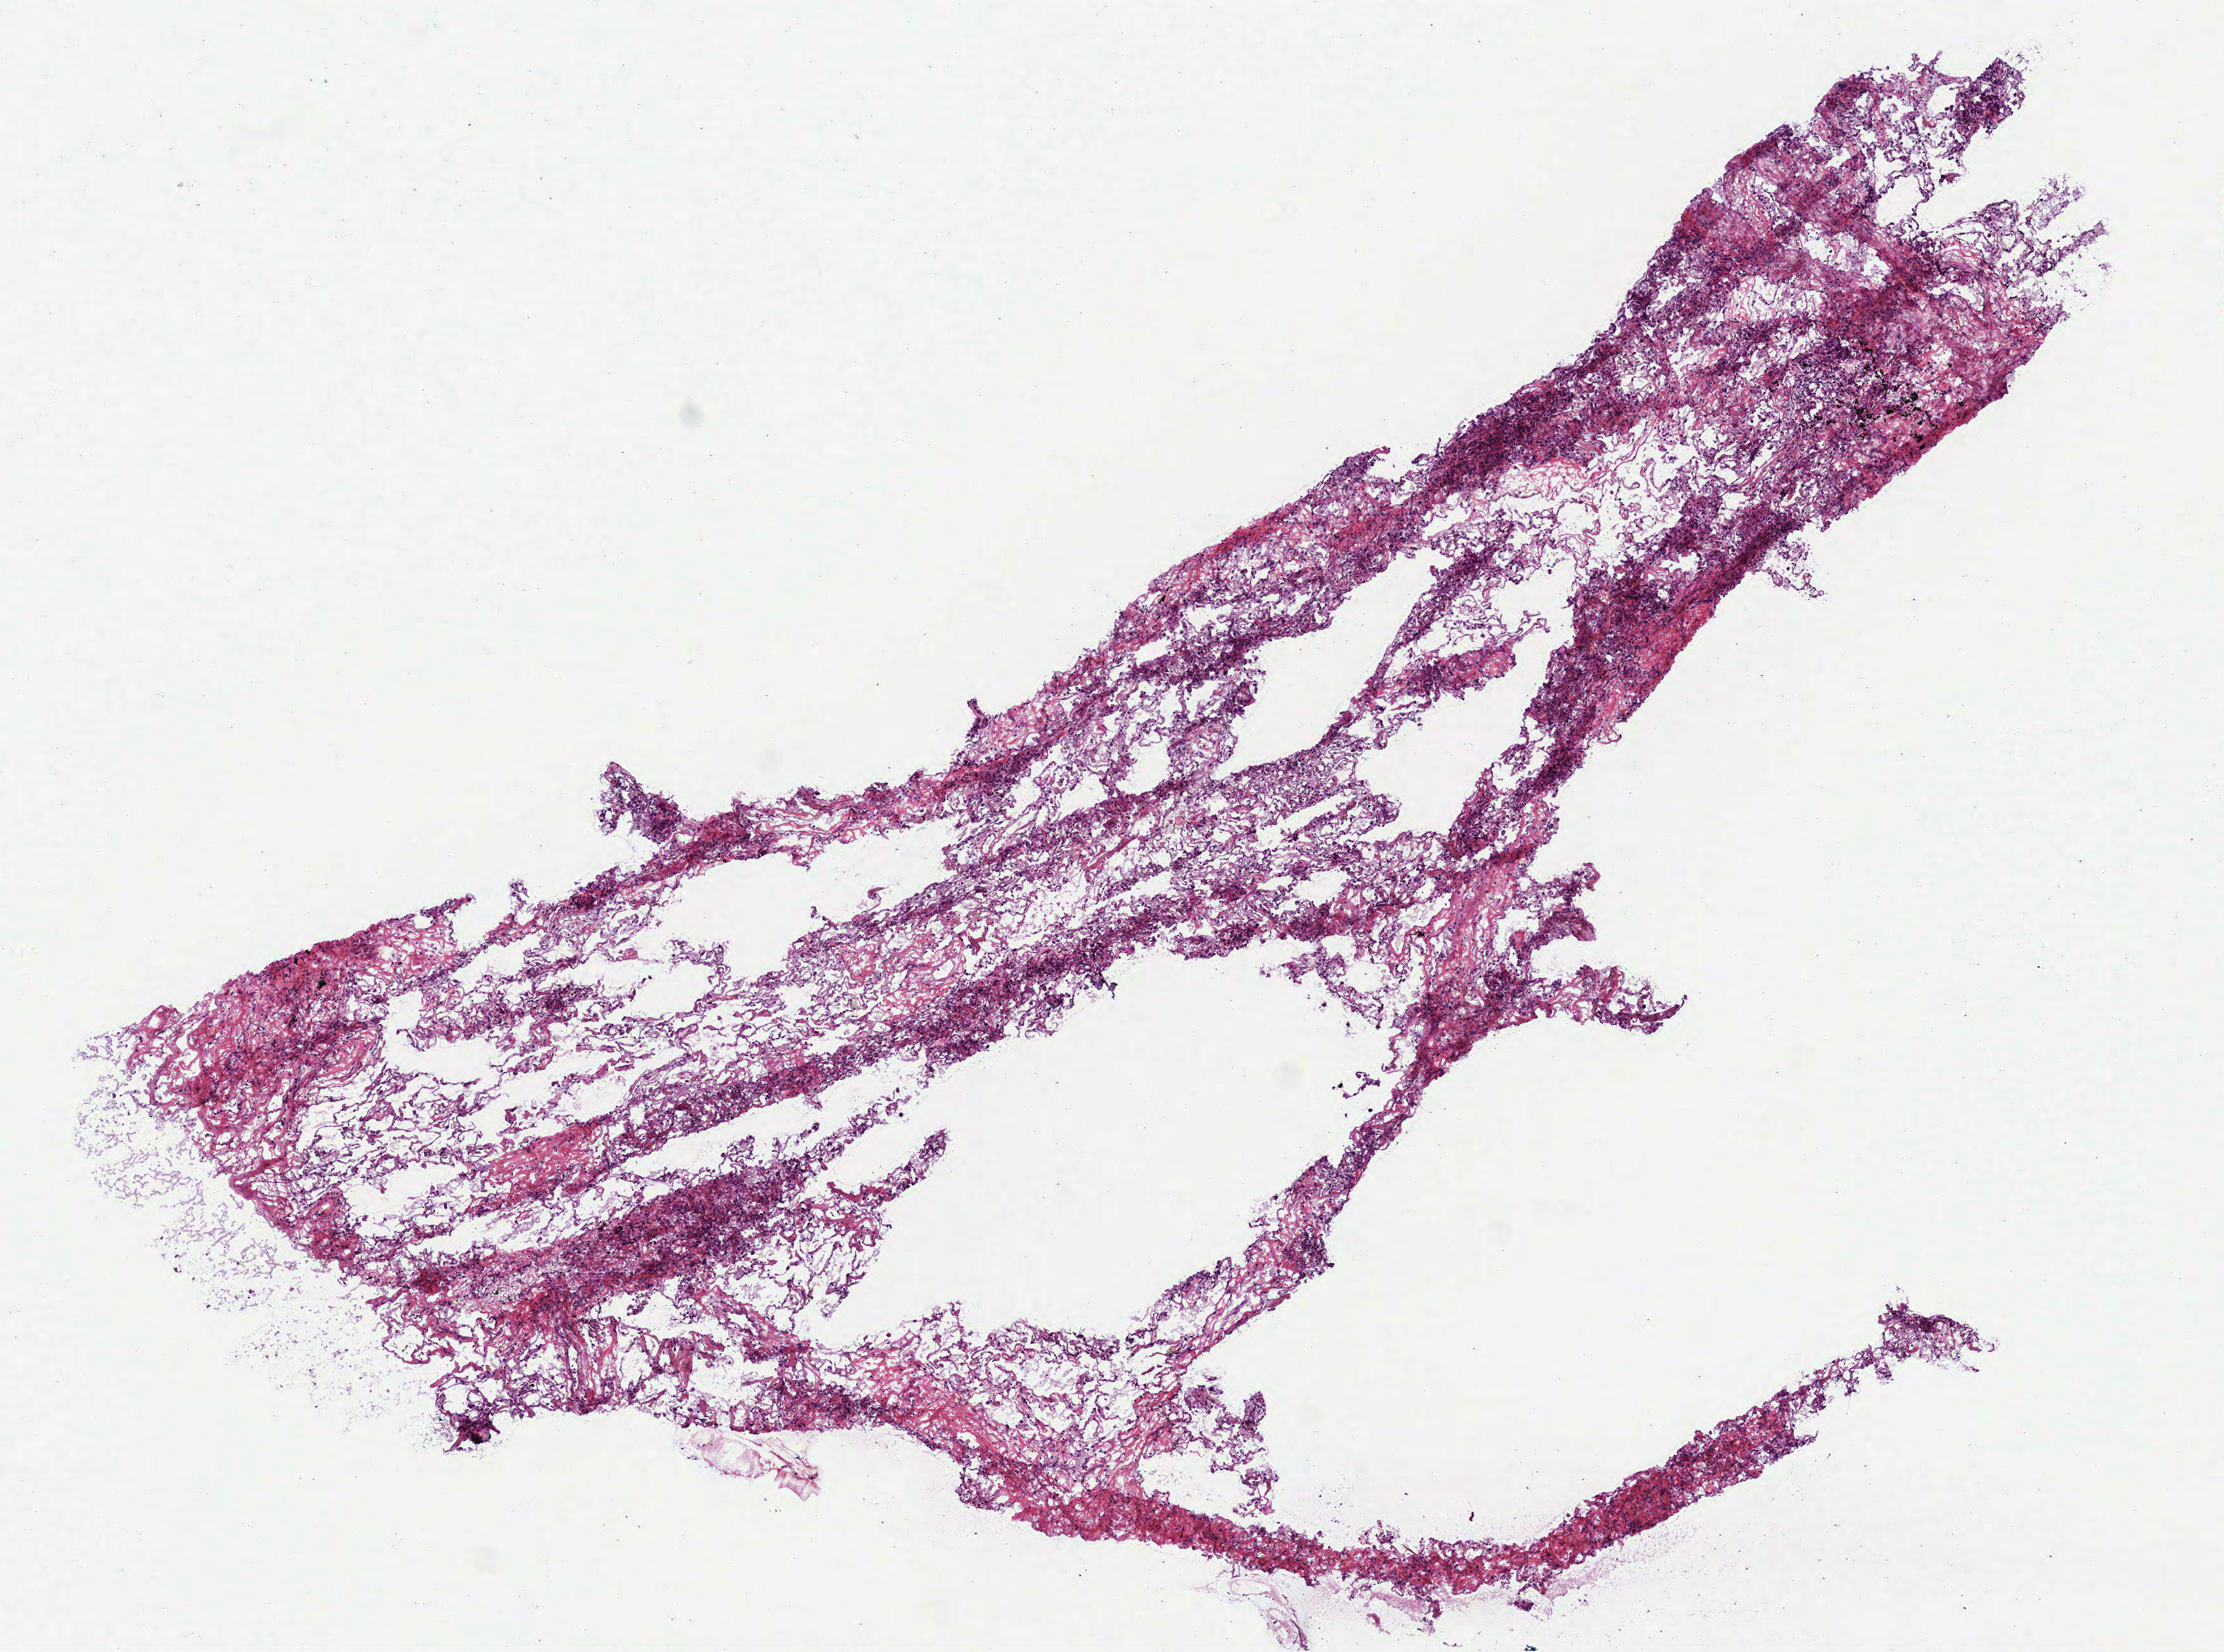
Digitized H&E tissue section (whole slide) — shown as a low-resolution overview of the whole scanned area (about 7.0 x 5.2 mm); frozen section; lung, solid tissue normal (non-tumour tissue) sample. Male patient; age at initial diagnosis 74 years.
This section: solid tissue normal (non-tumour) sample from the same patient. Patient diagnosis: Squamous cell carcinoma, NOS (upper lobe, lung).